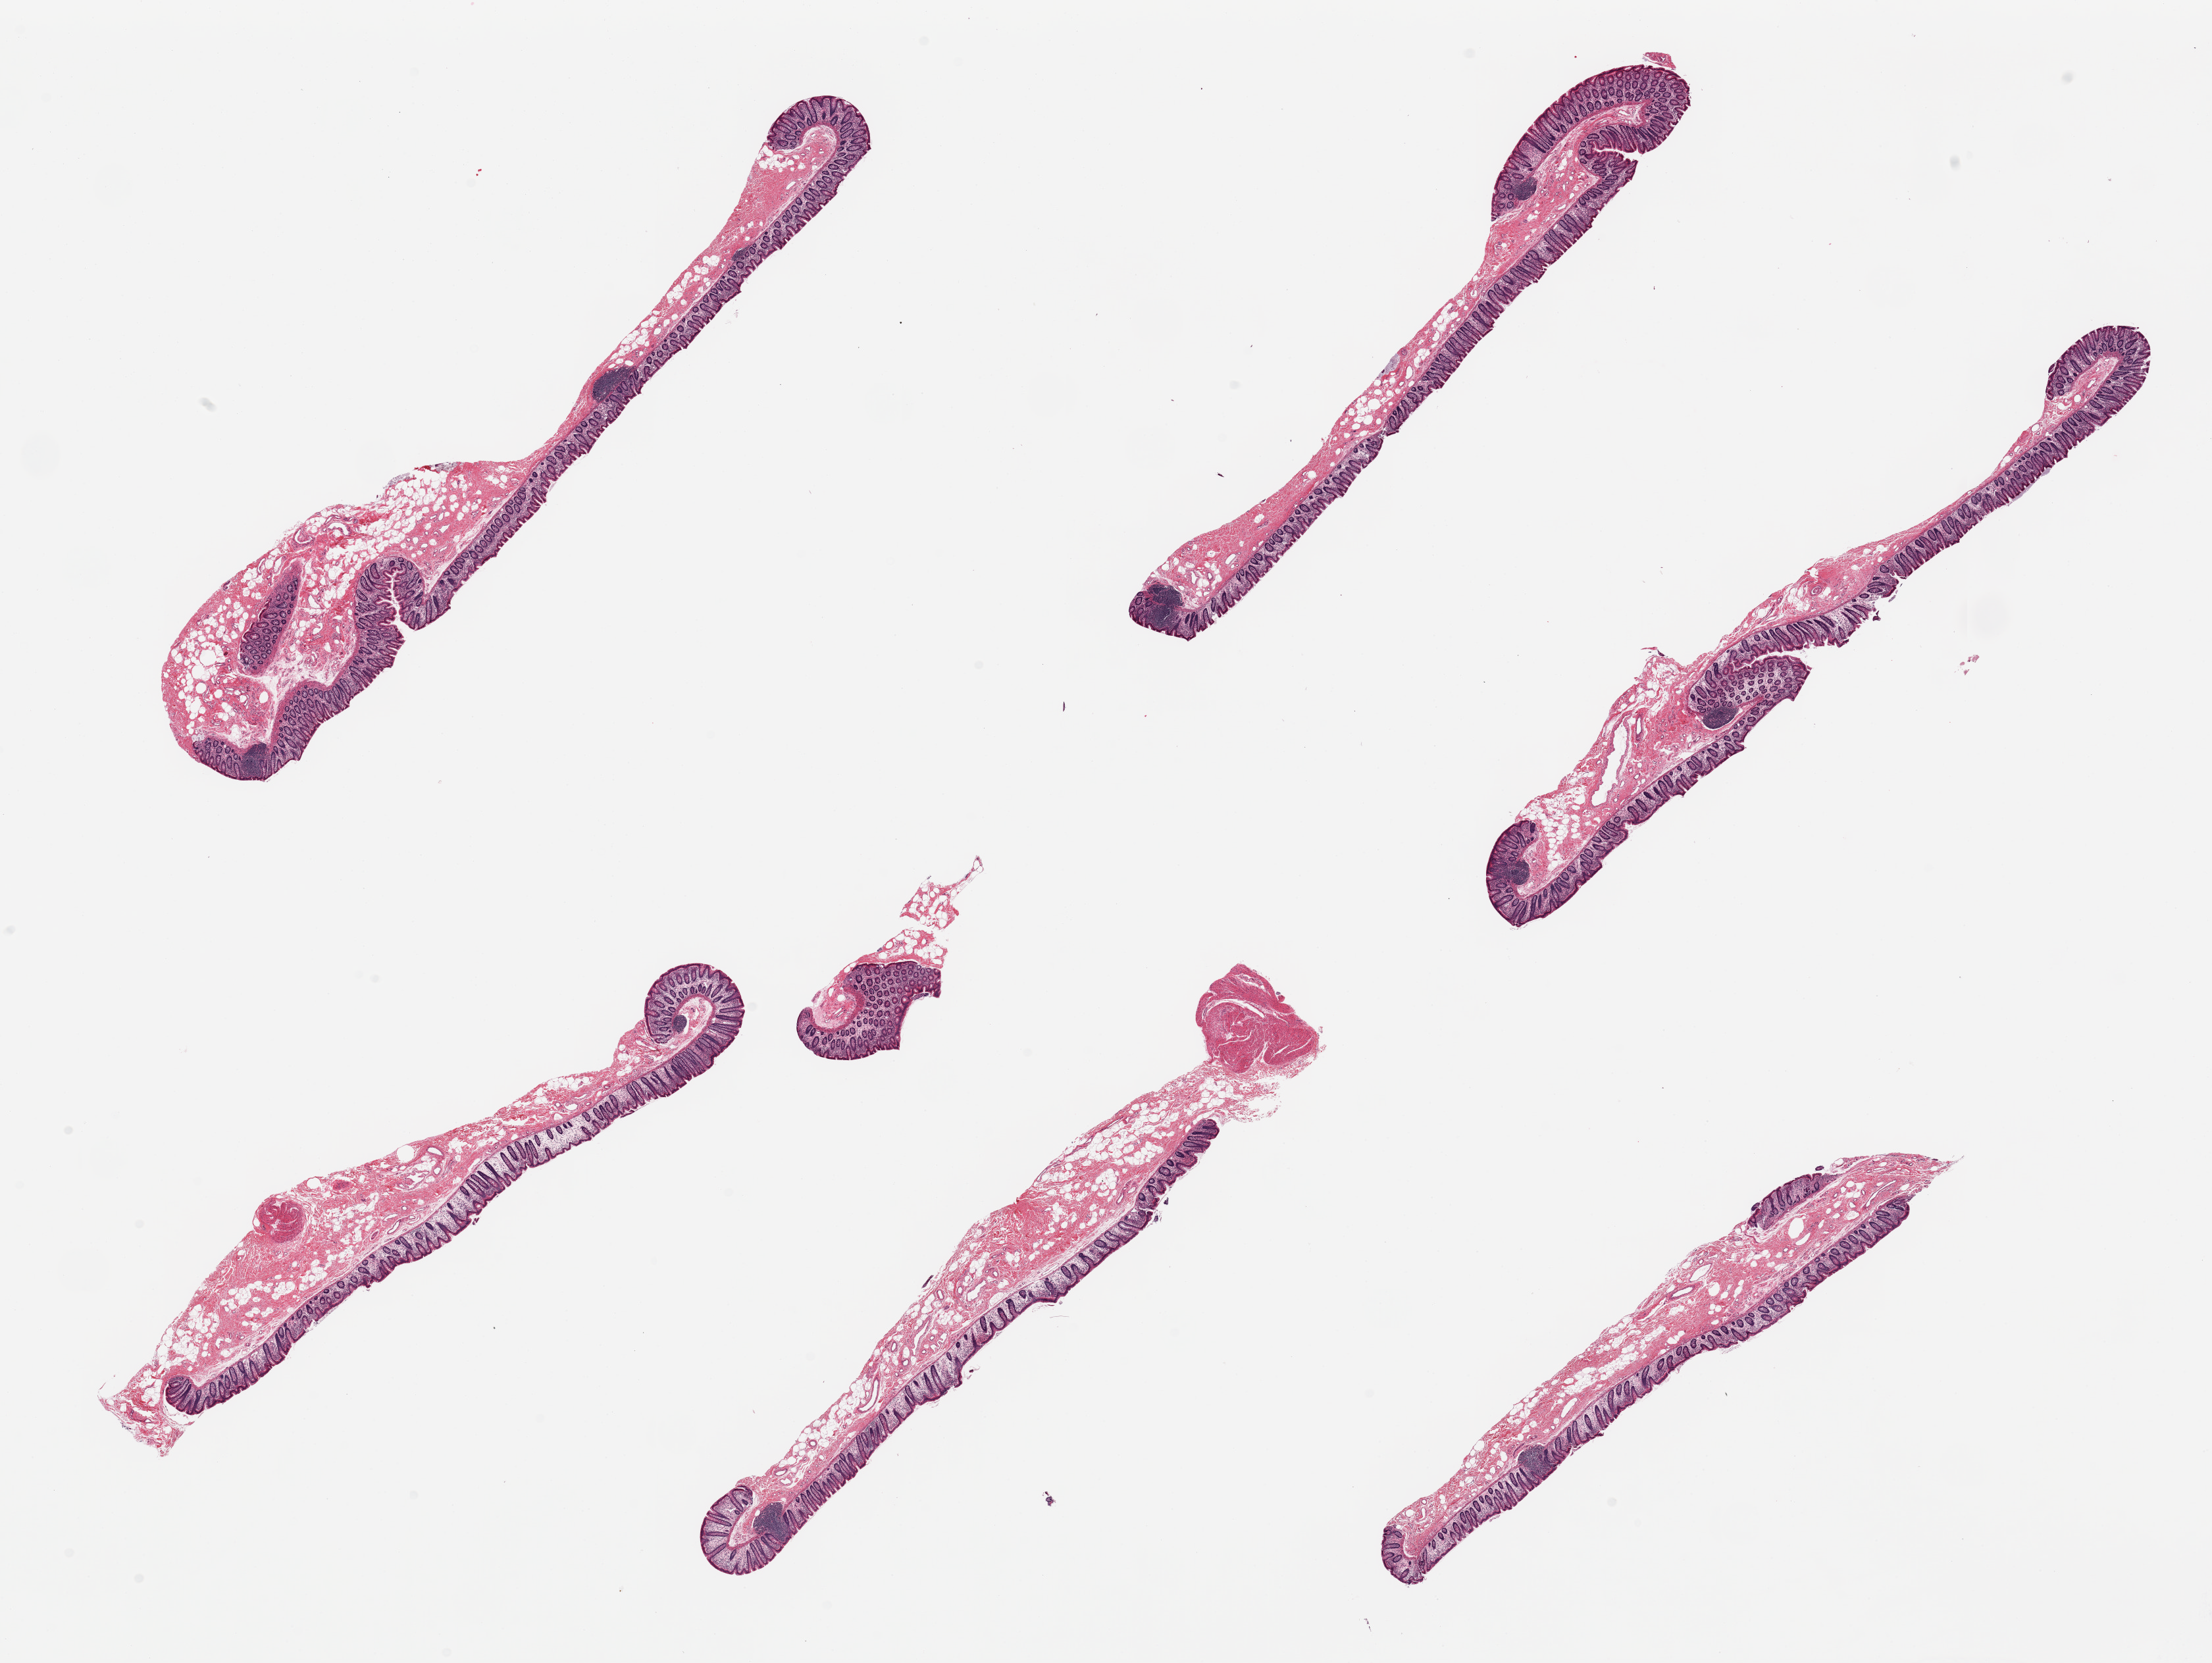
H&E whole-slide image — shown as a low-resolution overview of the whole scanned area (about 26.6 x 20.0 mm). PAXgene-fixed paraffin-embedded (PFPE) section. Section of transverse colon (target tissue). Tissue donor sample.
Pathologist's review note for this sample: 6 pieces, mucosa unusually well preserved, ~0.5mm, ~50% thickness.